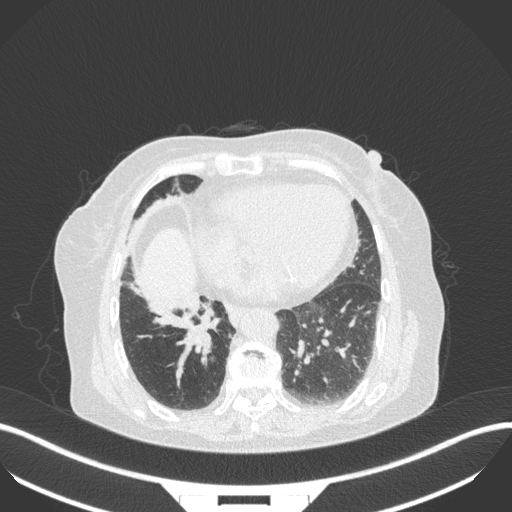
Chest CT, one axial slice; slice 110 of 329 in the series (ordered by position); lung window (W 1500 / L -600 HU); 1 mm slice thickness; 512 × 512 image matrix, field of view 400 × 400 mm. Patient: female, 75 years. Case-level facts recorded for this patient, not image findings: clinical TNM (as recorded): T1b N0 M1a; histopathological grade: G1.
Annotated regions visible in this slice (bounding box drawn by a radiologist):
- lung tumour (recorded histology: squamous cell carcinoma): bounding box <179,301,217,356> (left, top, right, bottom; pixels)